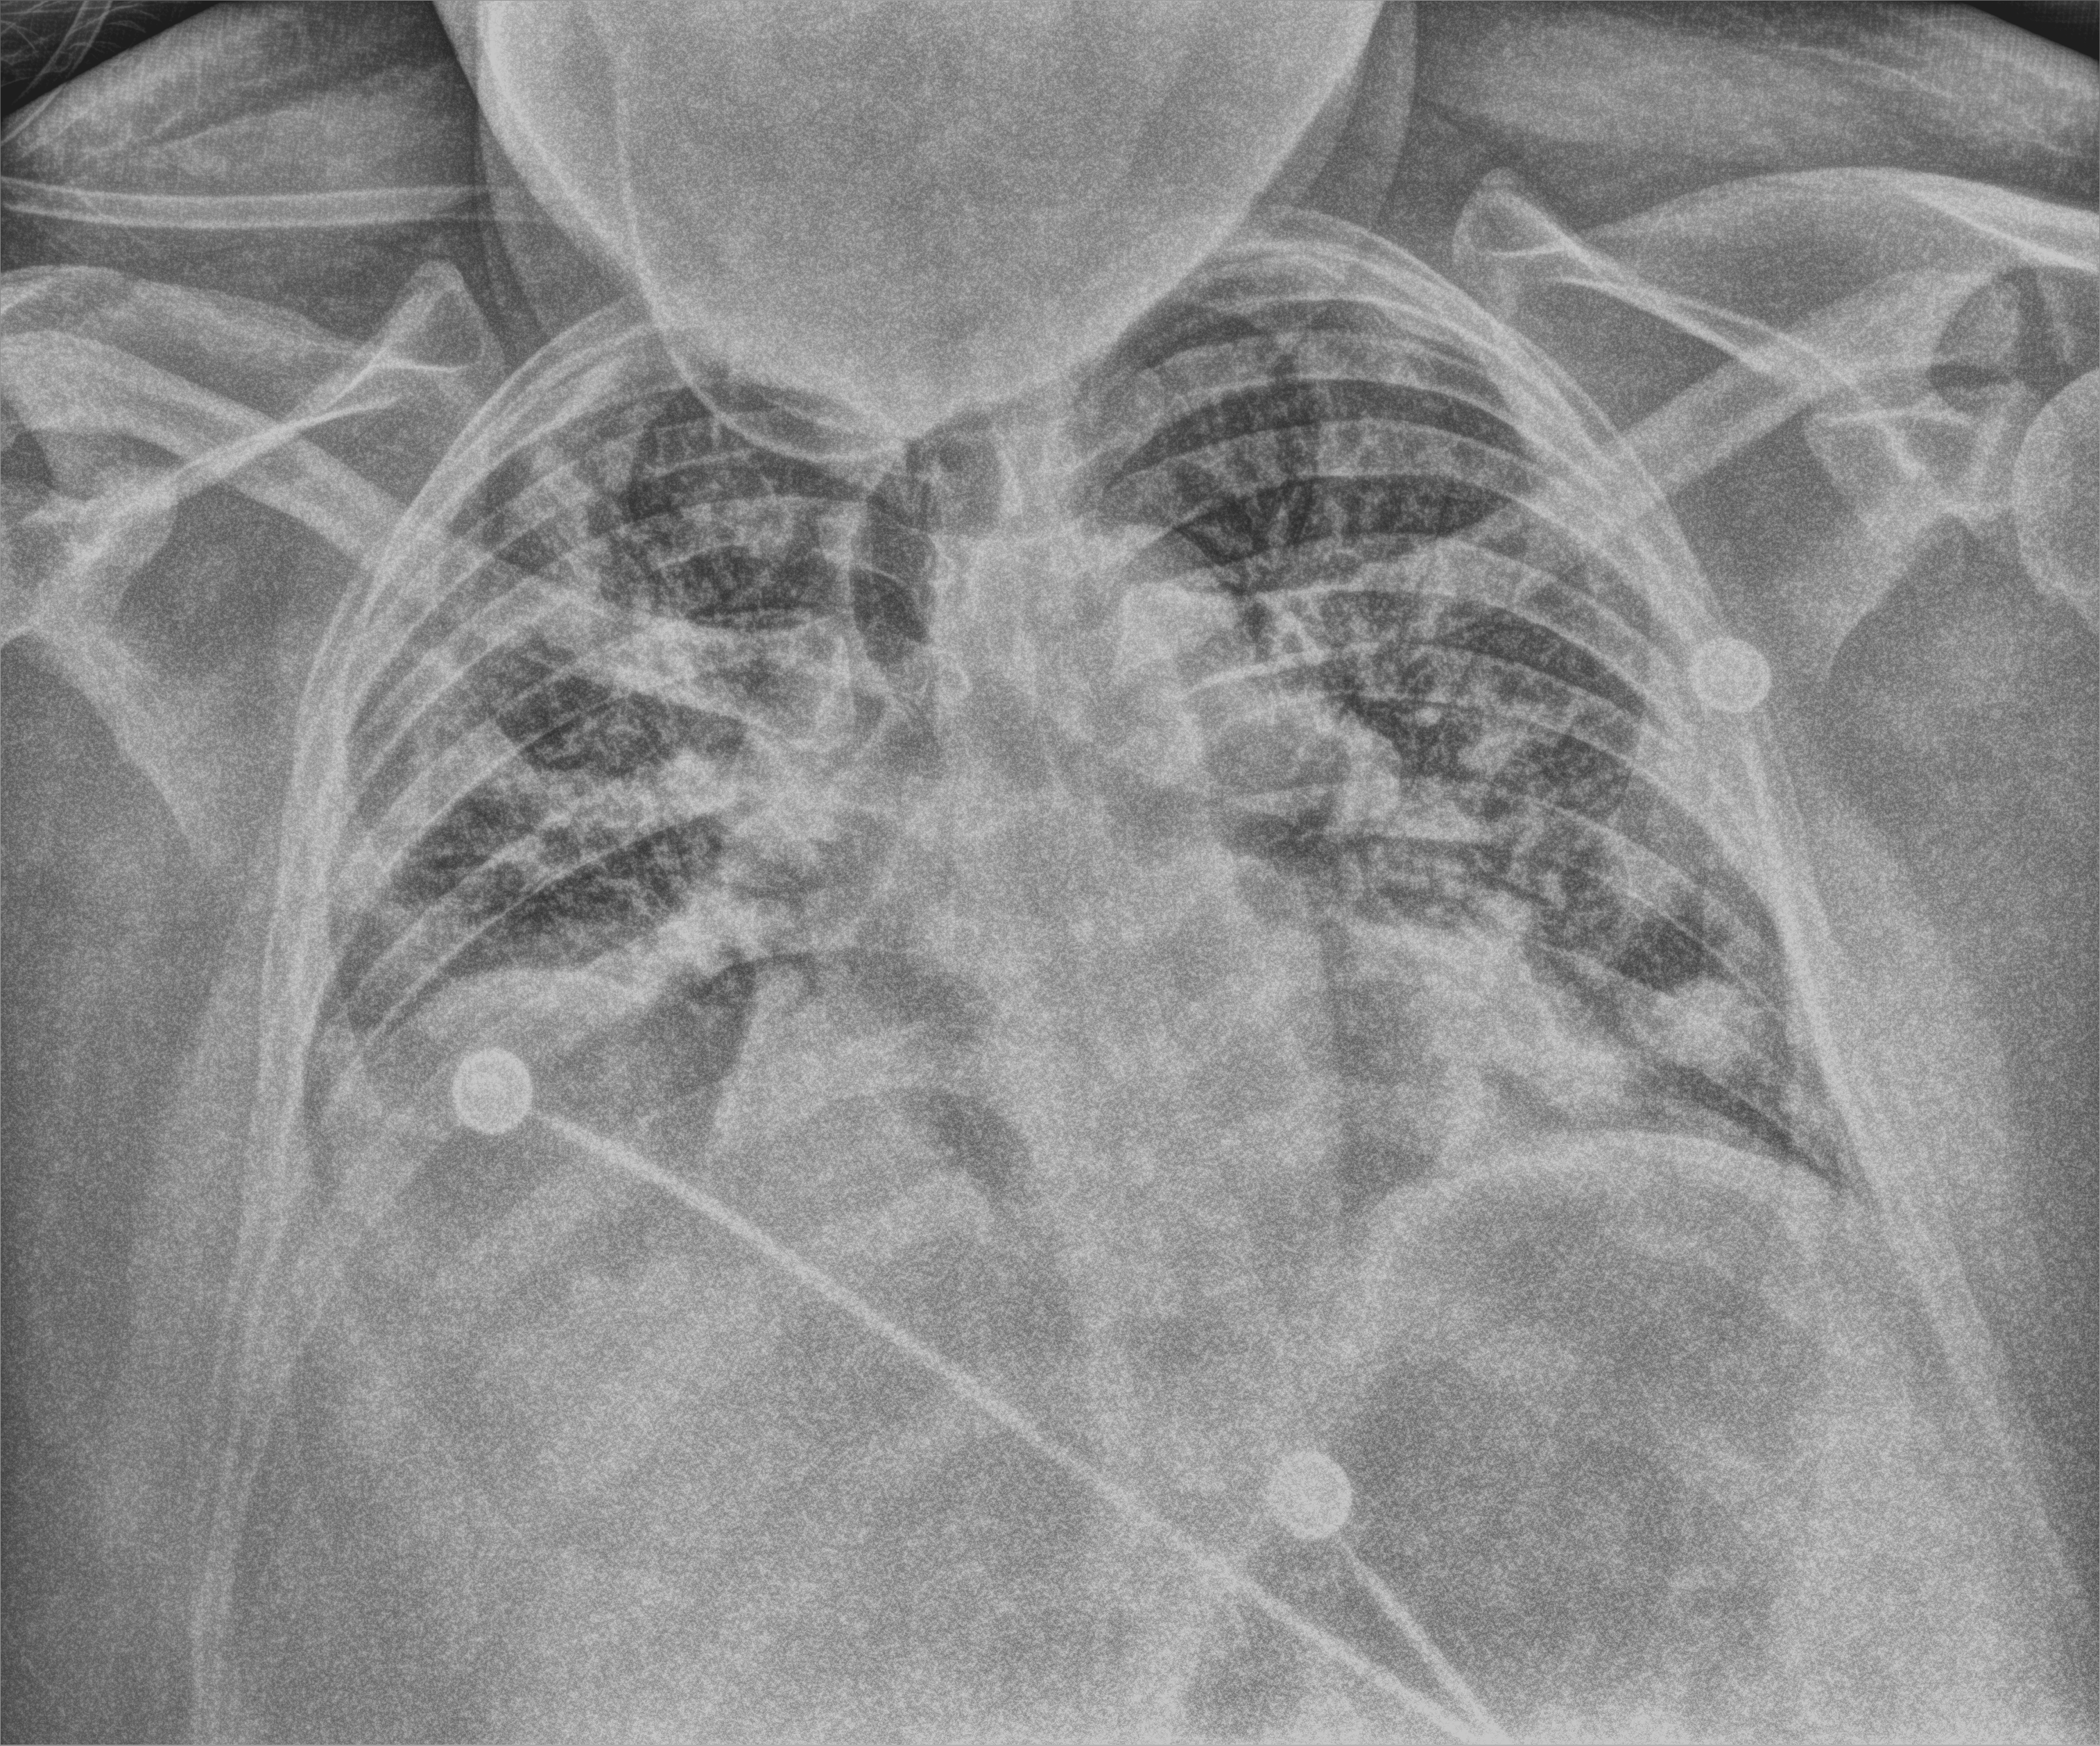
Bedside chest radiograph (computed radiography); anteroposterior (AP) projection. Patient hospitalised with COVID-19, aged 18–59 years.
From the hospital-stay record, not from the radiograph (when in the stay this image was taken is not recorded):
- admitted to intensive care during this hospital stay: yes